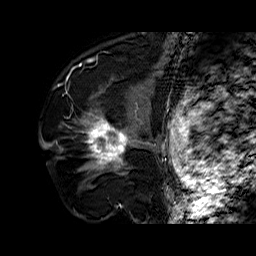
Breast MRI (dynamic contrast-enhanced), one sagittal slice. Position 41 of 60 along the scan axis. Dynamic contrast-enhanced series, time point 2 of 6 at this slice position (early post-contrast). 1.5 T. TE 6.4 ms, TR 32.7 ms. 256 × 256 image matrix. Female patient. From the clinical record (not read from this slice): setting: breast cancer imaged before/during neoadjuvant chemotherapy; receptor status: HR-positive, HER2-negative.
Structures marked on this image (semi-automatically segmented with operator editing):
- analysis volume of interest (the breast-tissue region the enhancement analysis was run in; not a lesion): bounding box [x1, y1, x2, y2] px = [74, 110, 141, 179]
- tumour enhancement mask (voxels above the 100 % enhancement threshold inside the analysis volume of interest): [85, 116, 131, 168]